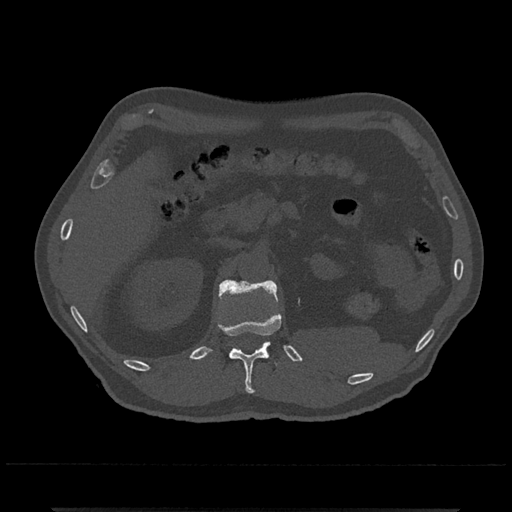
CT including the spine, one axial slice; slice 410 of 797 in the series (ordered by position); bone window (W 1800 / L 400 HU); 512 × 512 image matrix, field of view 393 × 393 mm. Patient: male, 67 years. From the clinical record (not read from this slice): primary cancer: prostate.
Annotated regions visible in this slice (semi-automatic segmentation, software-assisted and operator-edited):
- L1 vertebra: bounding box [x1, y1, x2, y2] px = [219, 279, 278, 355]
- T12 vertebra: [219, 293, 282, 394]